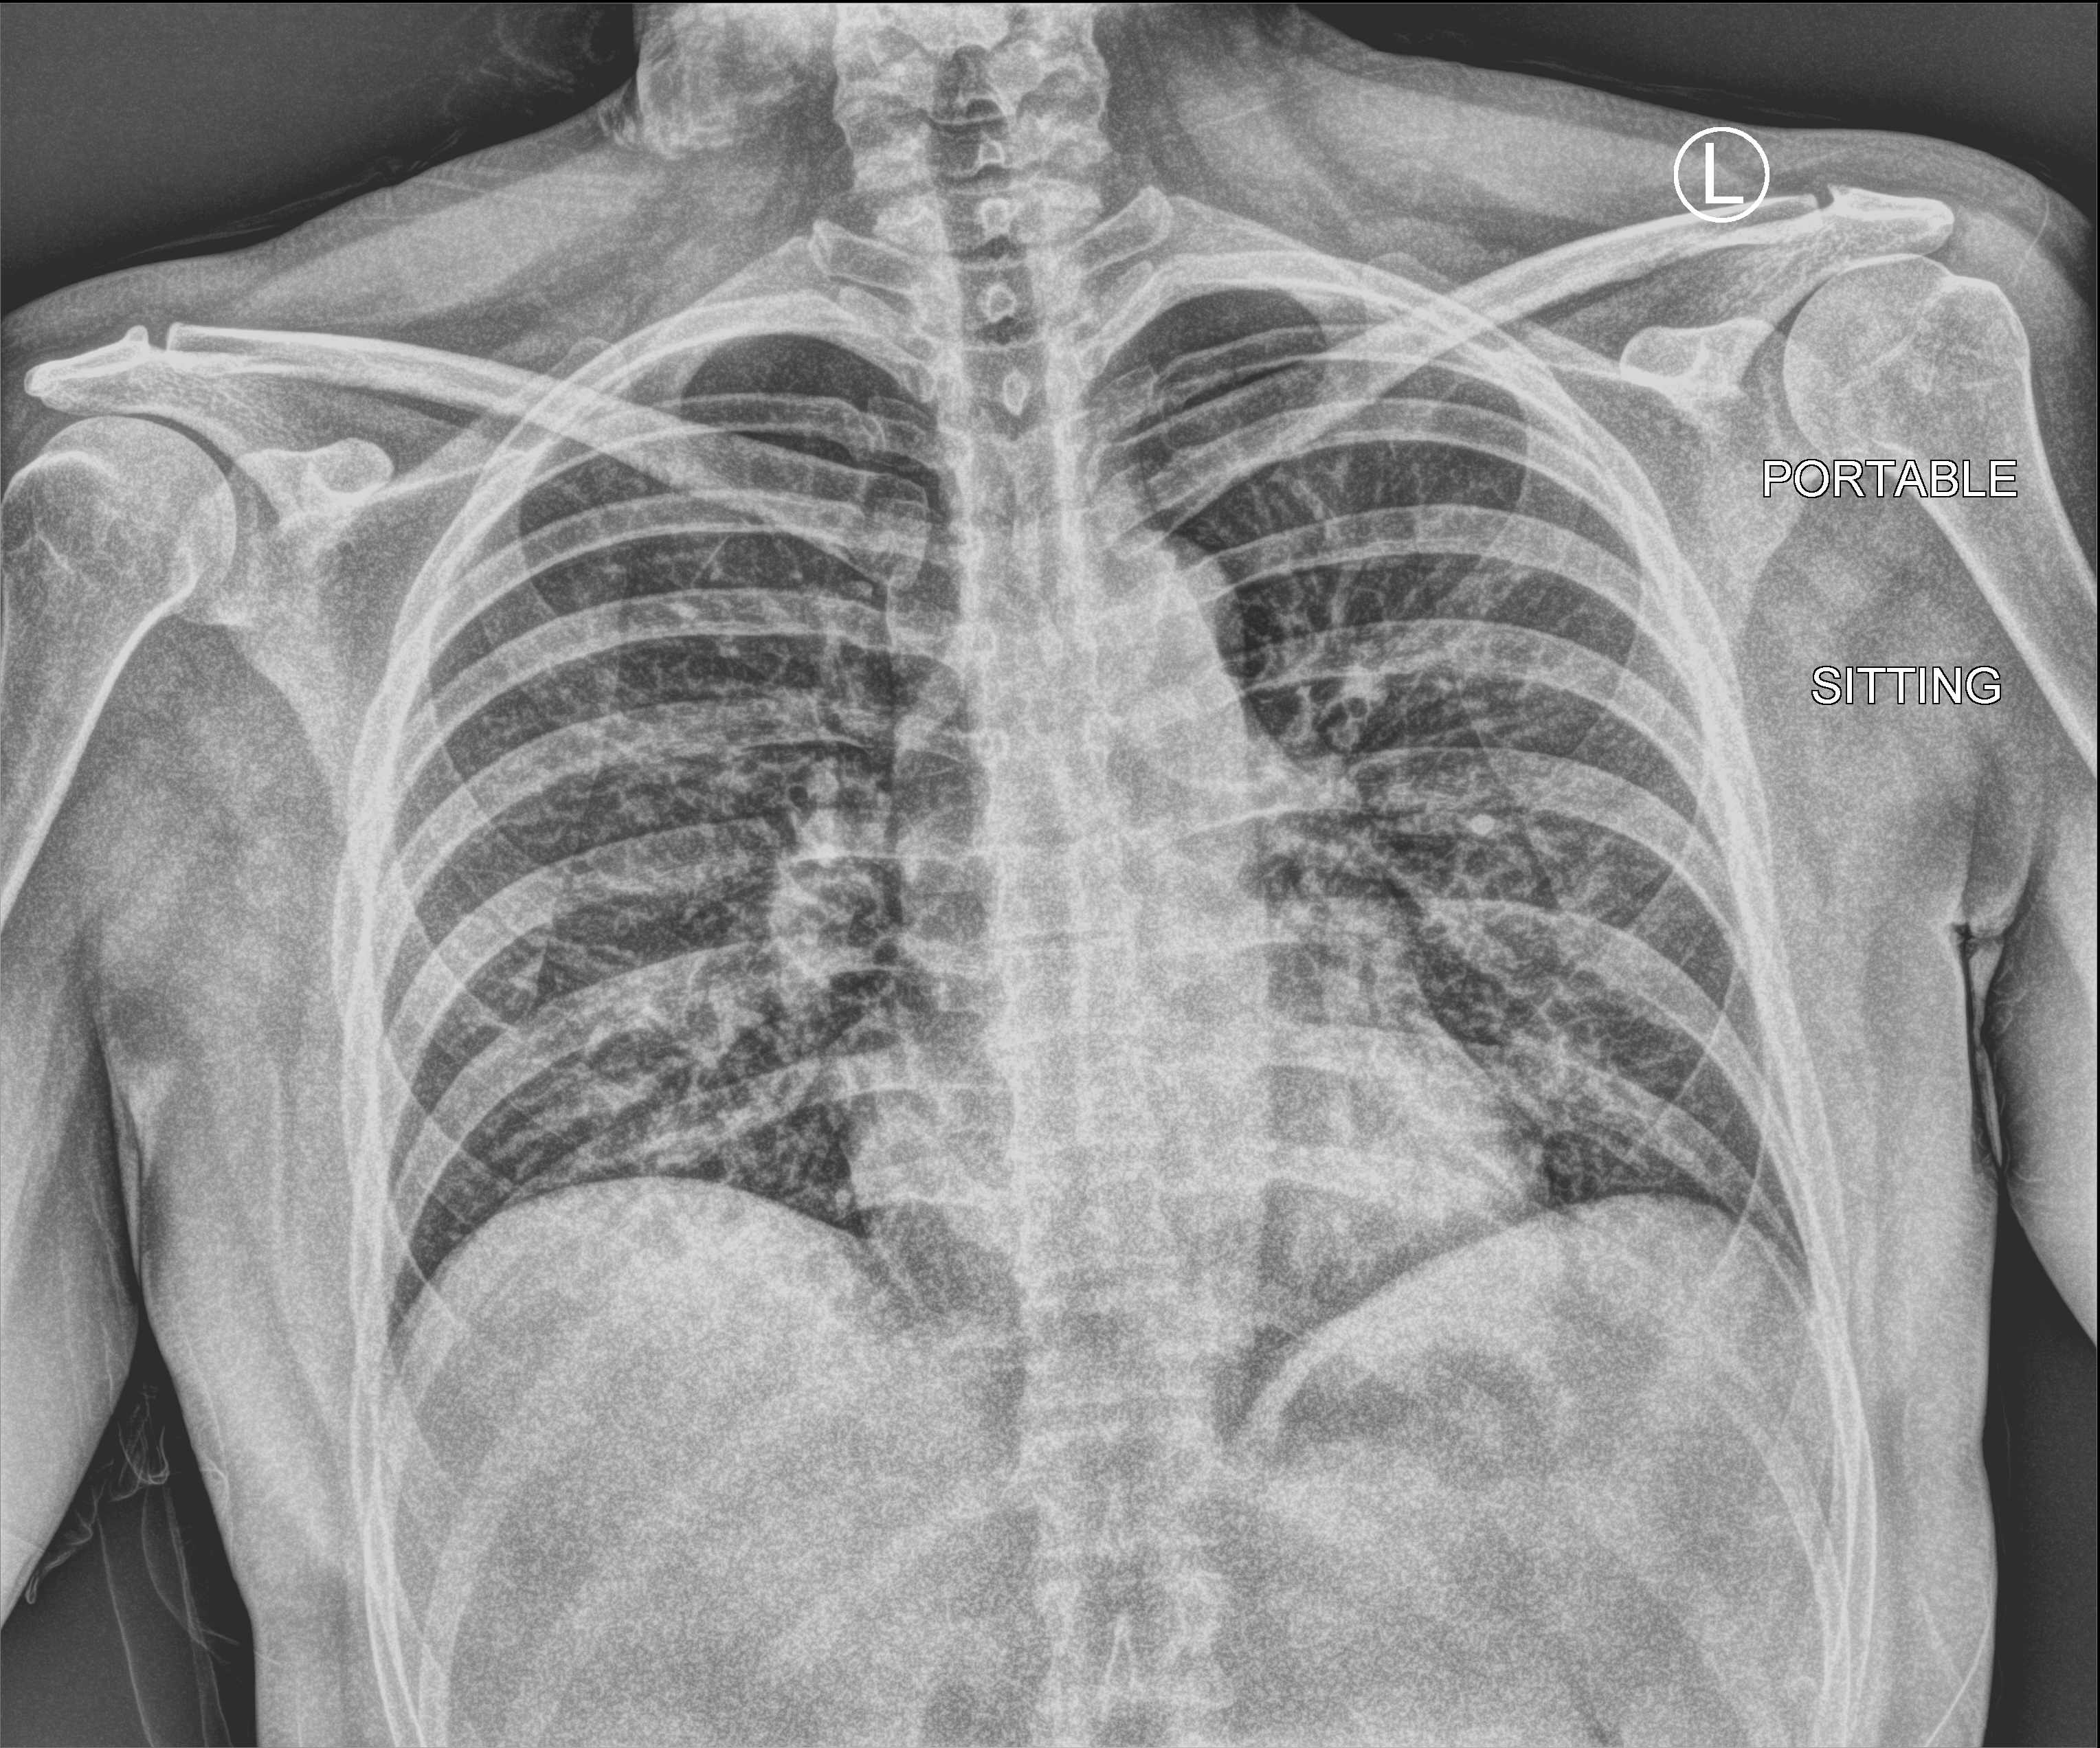
Chest X-ray (portable), anteroposterior (AP) projection. Patient hospitalised with COVID-19; female, aged 18–59 years.
Hospital-stay facts (about this admission, not read from this image; timing relative to this image not recorded):
- diabetes (admission record): no
- mechanically ventilated during this hospital stay: no
- admitted to intensive care during this hospital stay: no